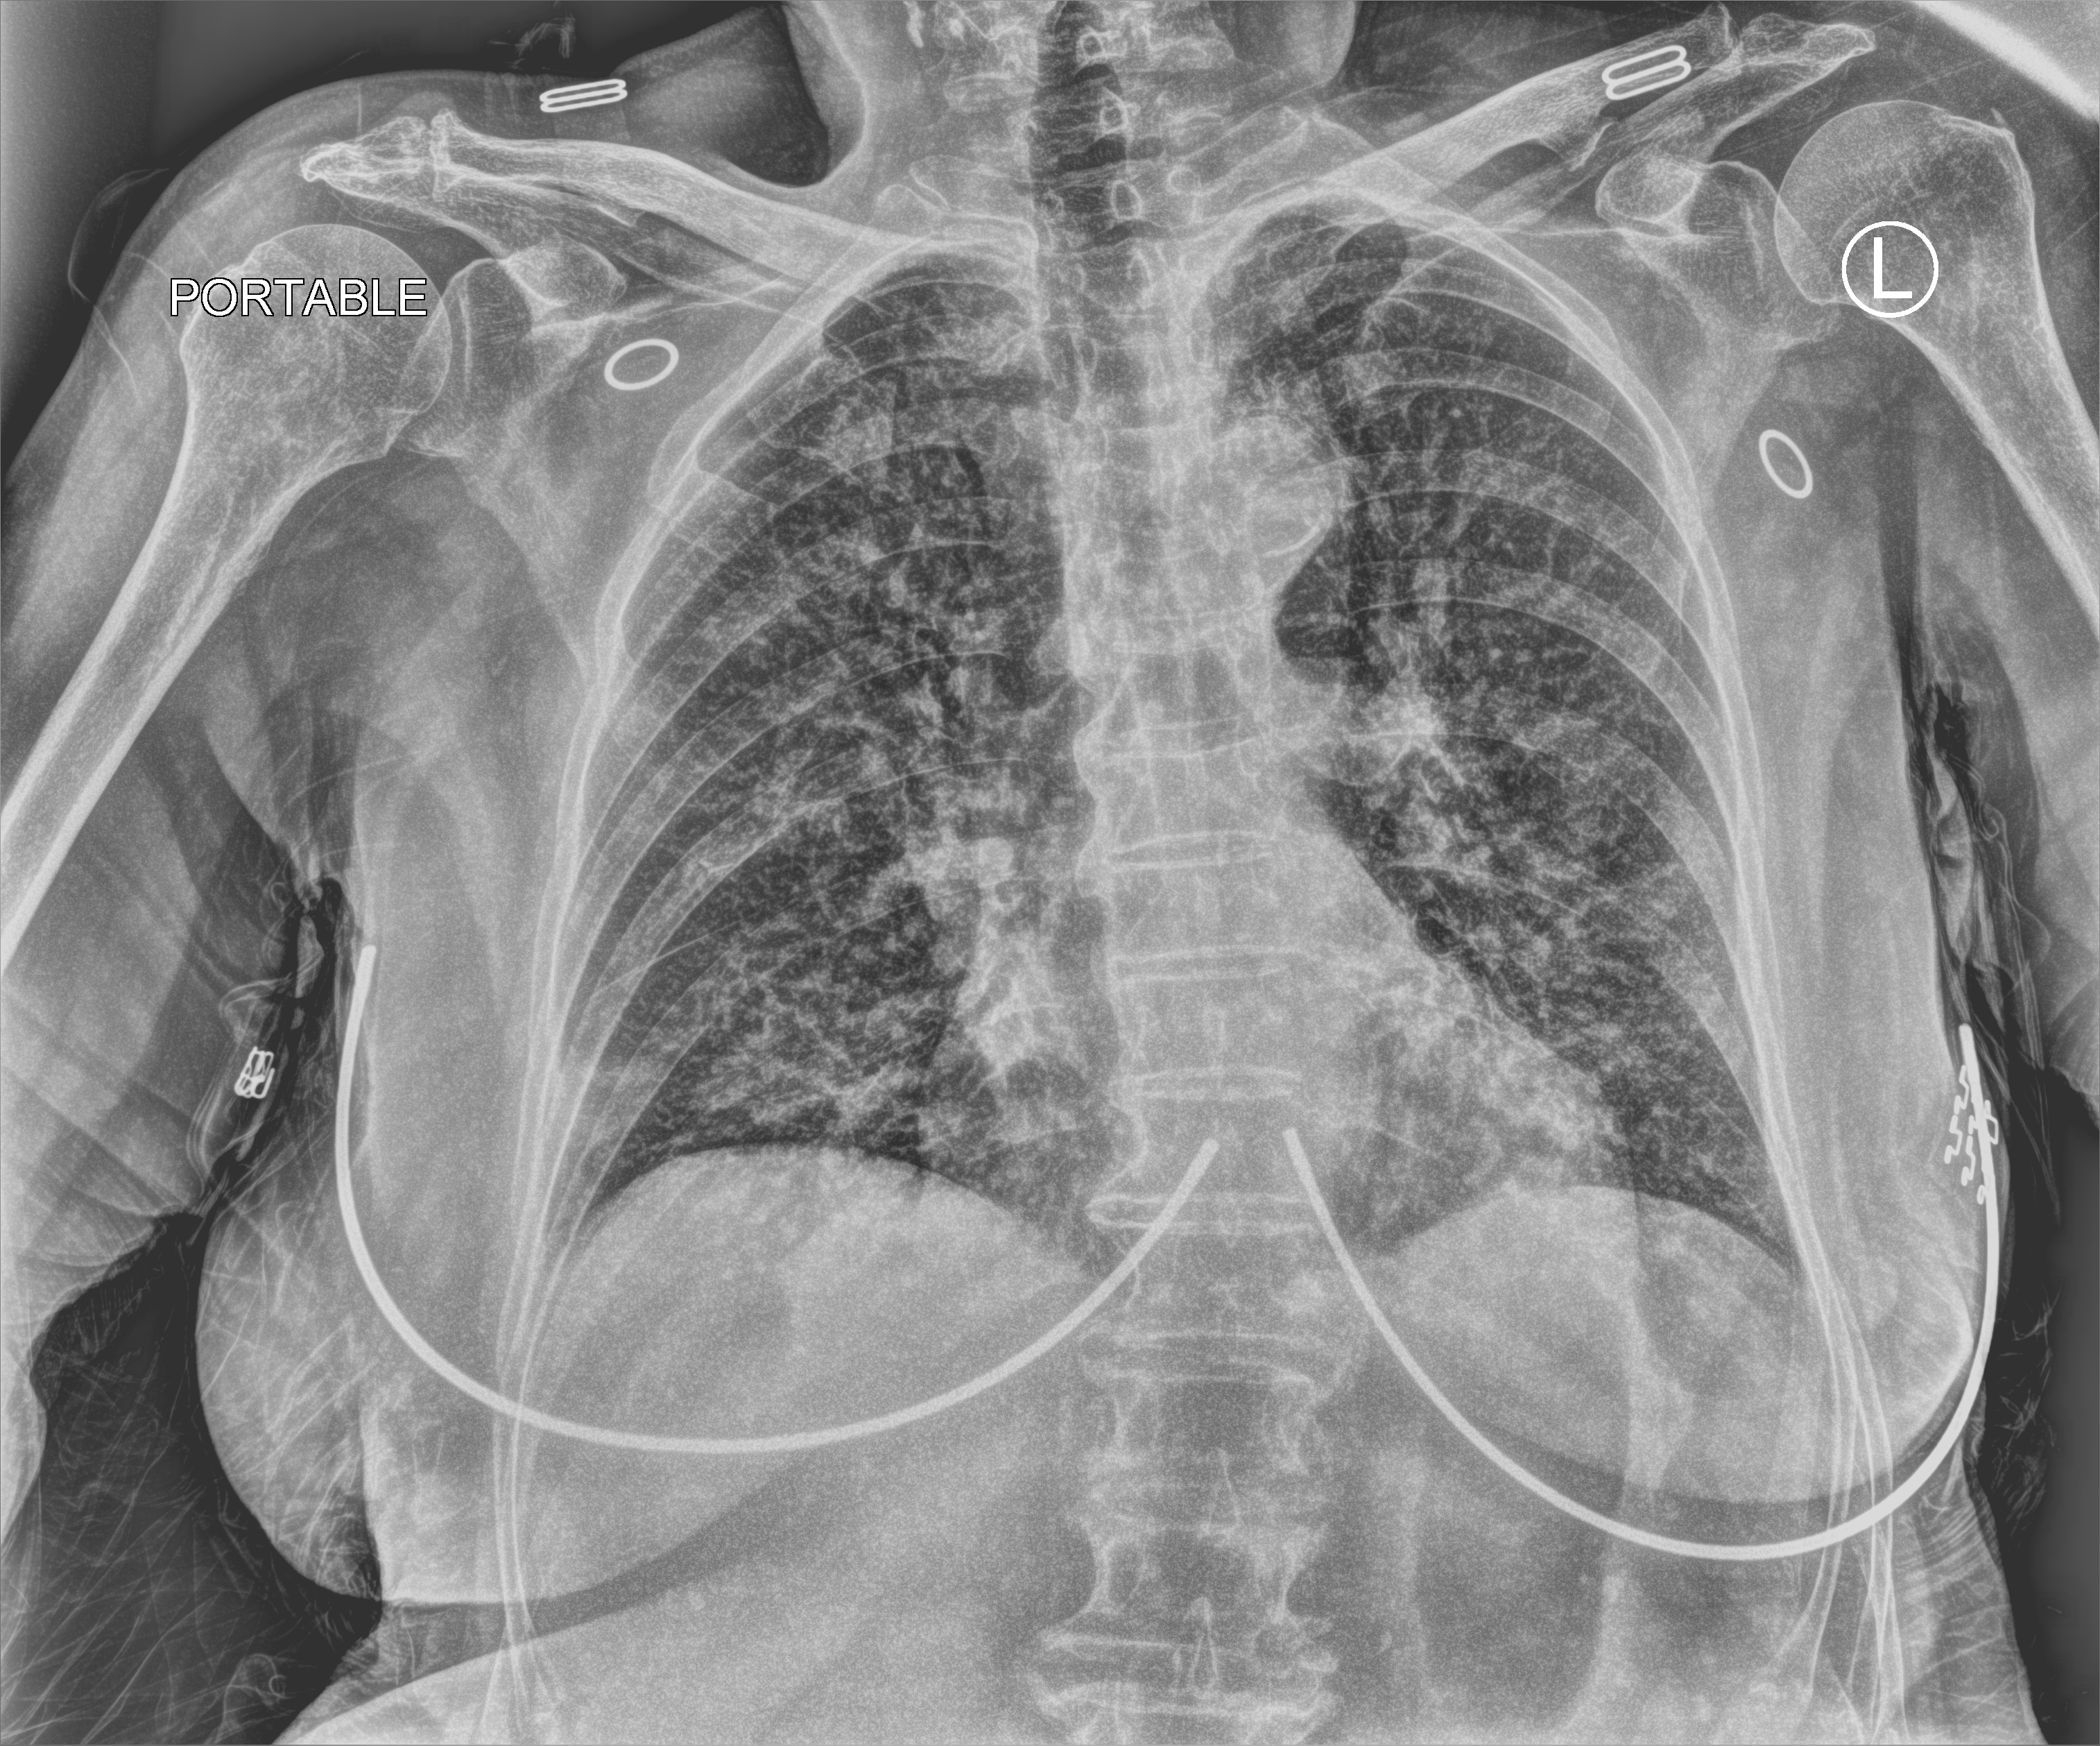
Portable chest radiograph, anteroposterior (AP) projection. Patient hospitalised with COVID-19; female, aged 75–90 years.
From the hospital-stay record, not from the radiograph (when in the stay this image was taken is not recorded):
- admitted to intensive care during this hospital stay: no
- mechanically ventilated during this hospital stay: no